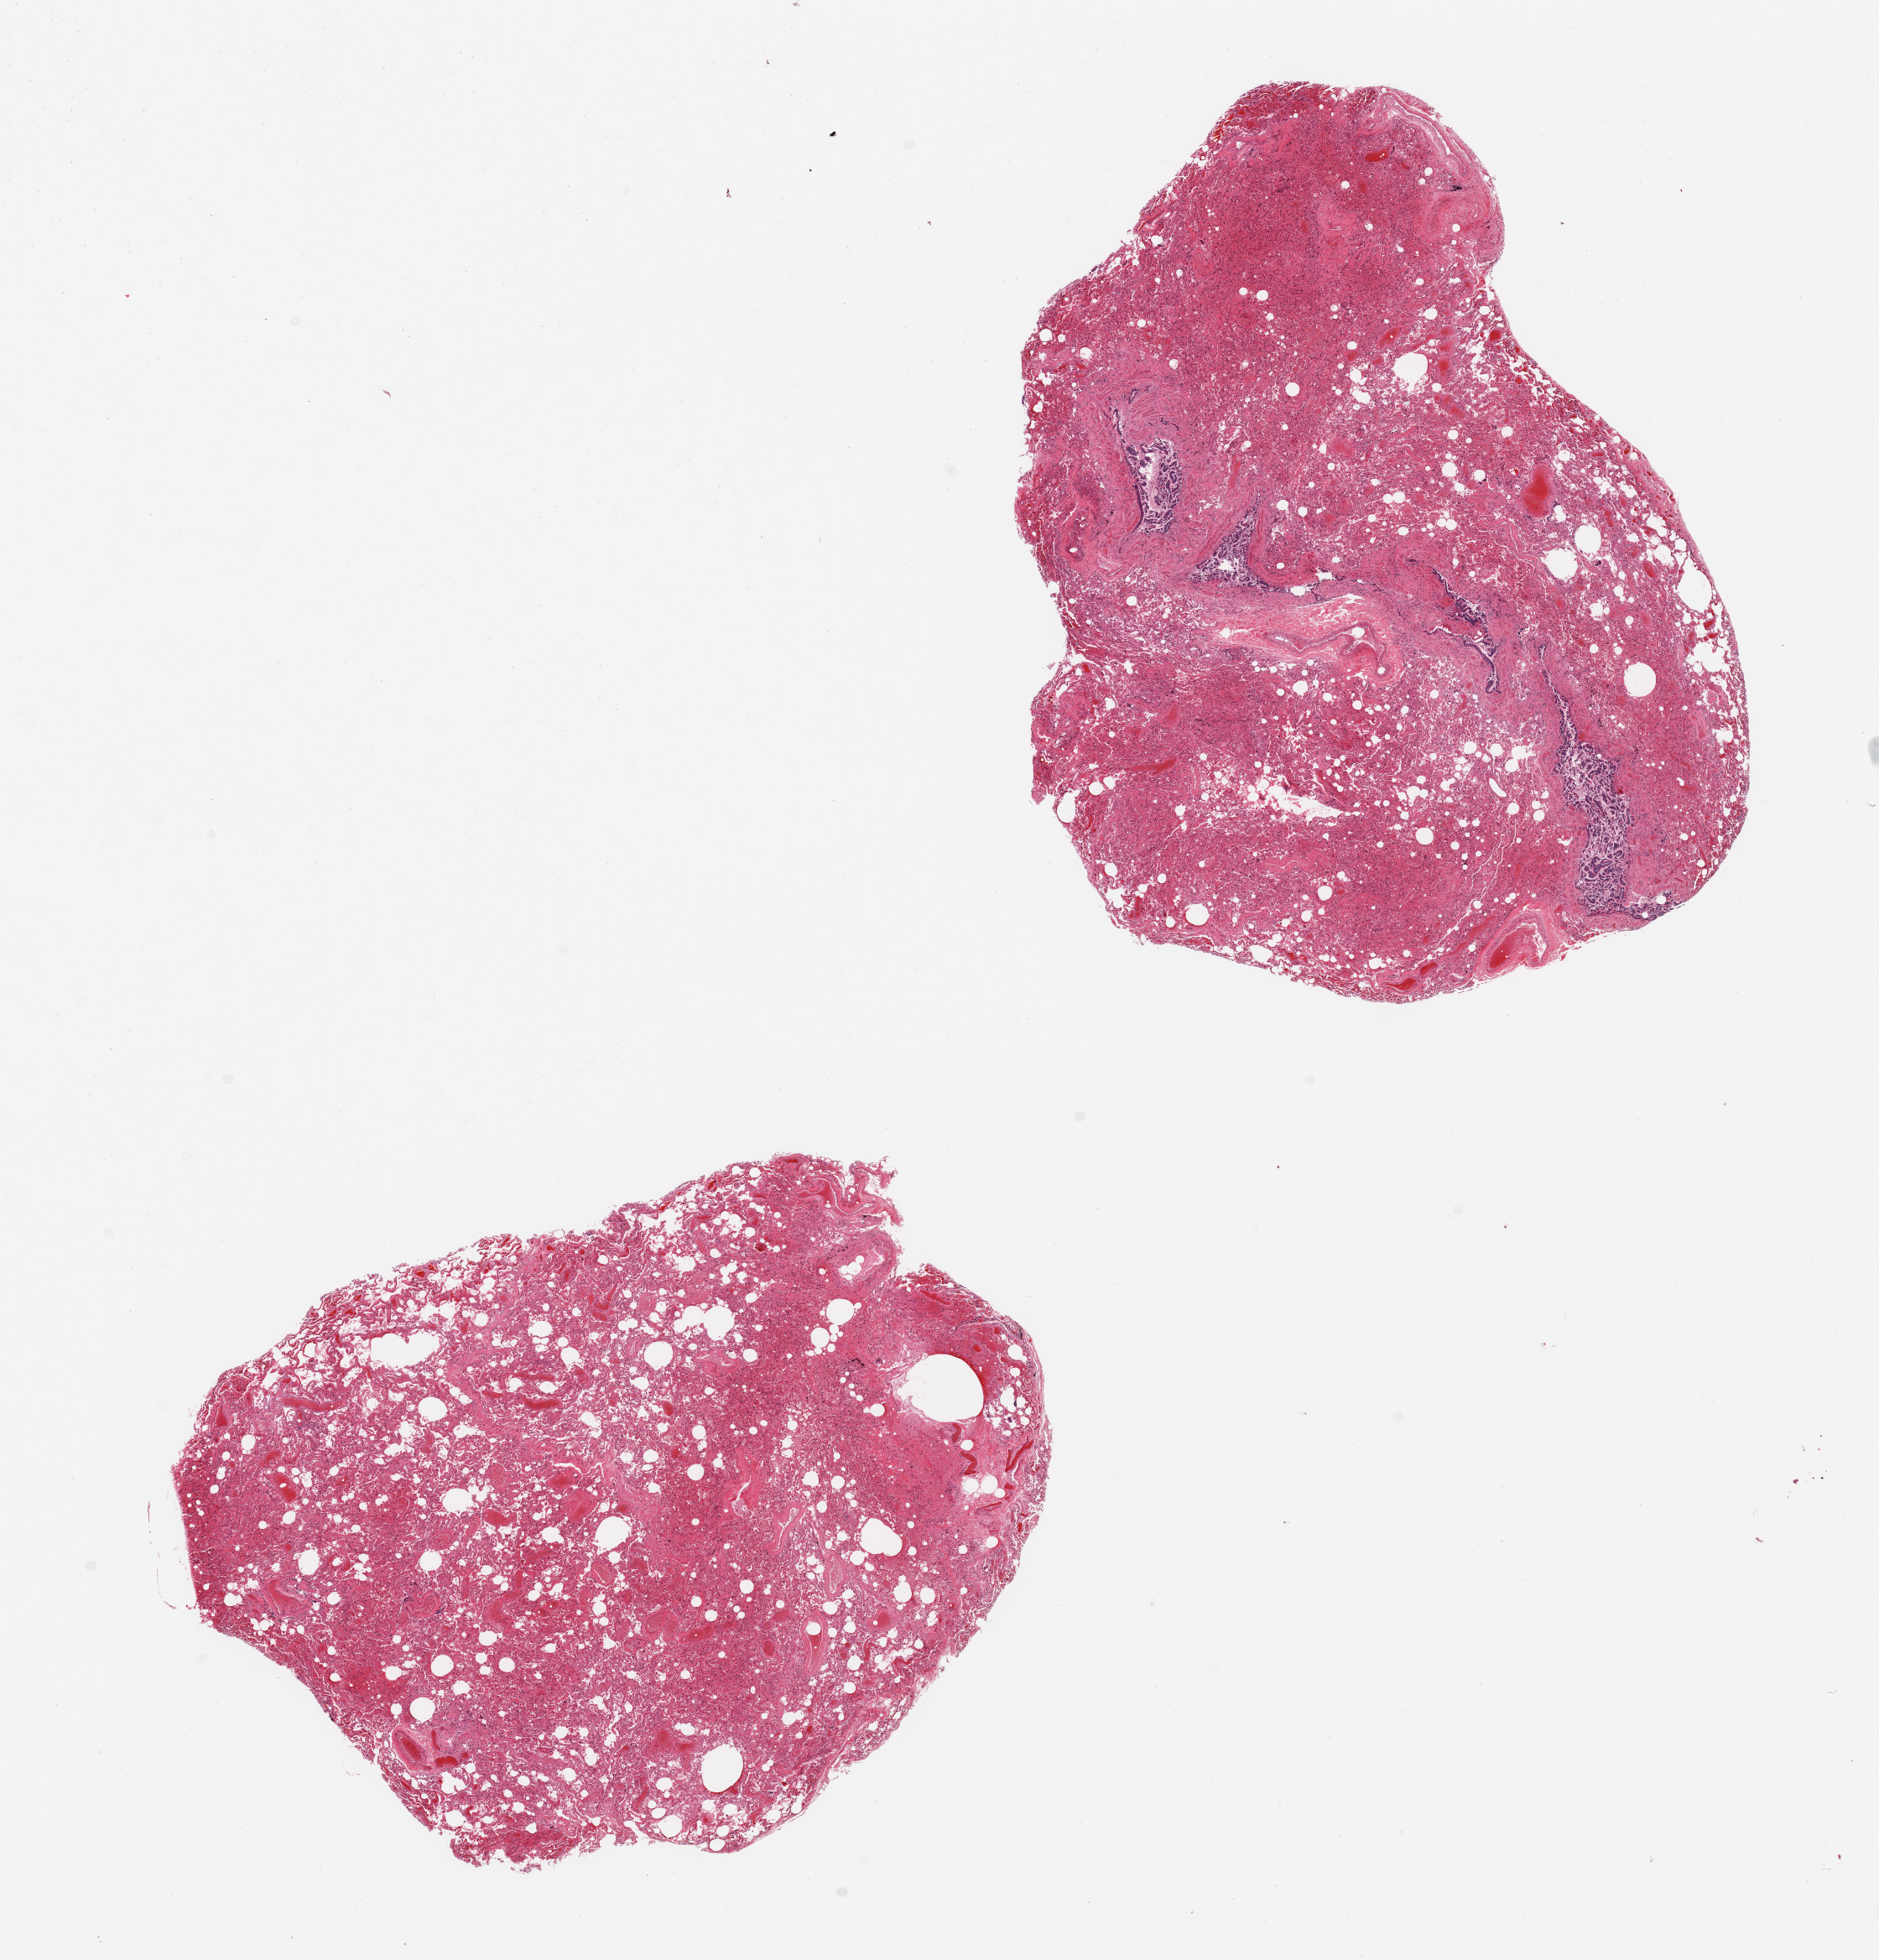
Haematoxylin and eosin whole-slide image — whole scanned area (about 17.7 x 18.5 mm) shown as a low-resolution overview; PAXgene-fixed, paraffin-embedded tissue; section of lung (target tissue); tissue donor sample. Male donor.
Pathologist's review note for this sample: 2 pieces, congestion, intra-alveolar hemorrhage, and sloughing of bronchial epithelium.